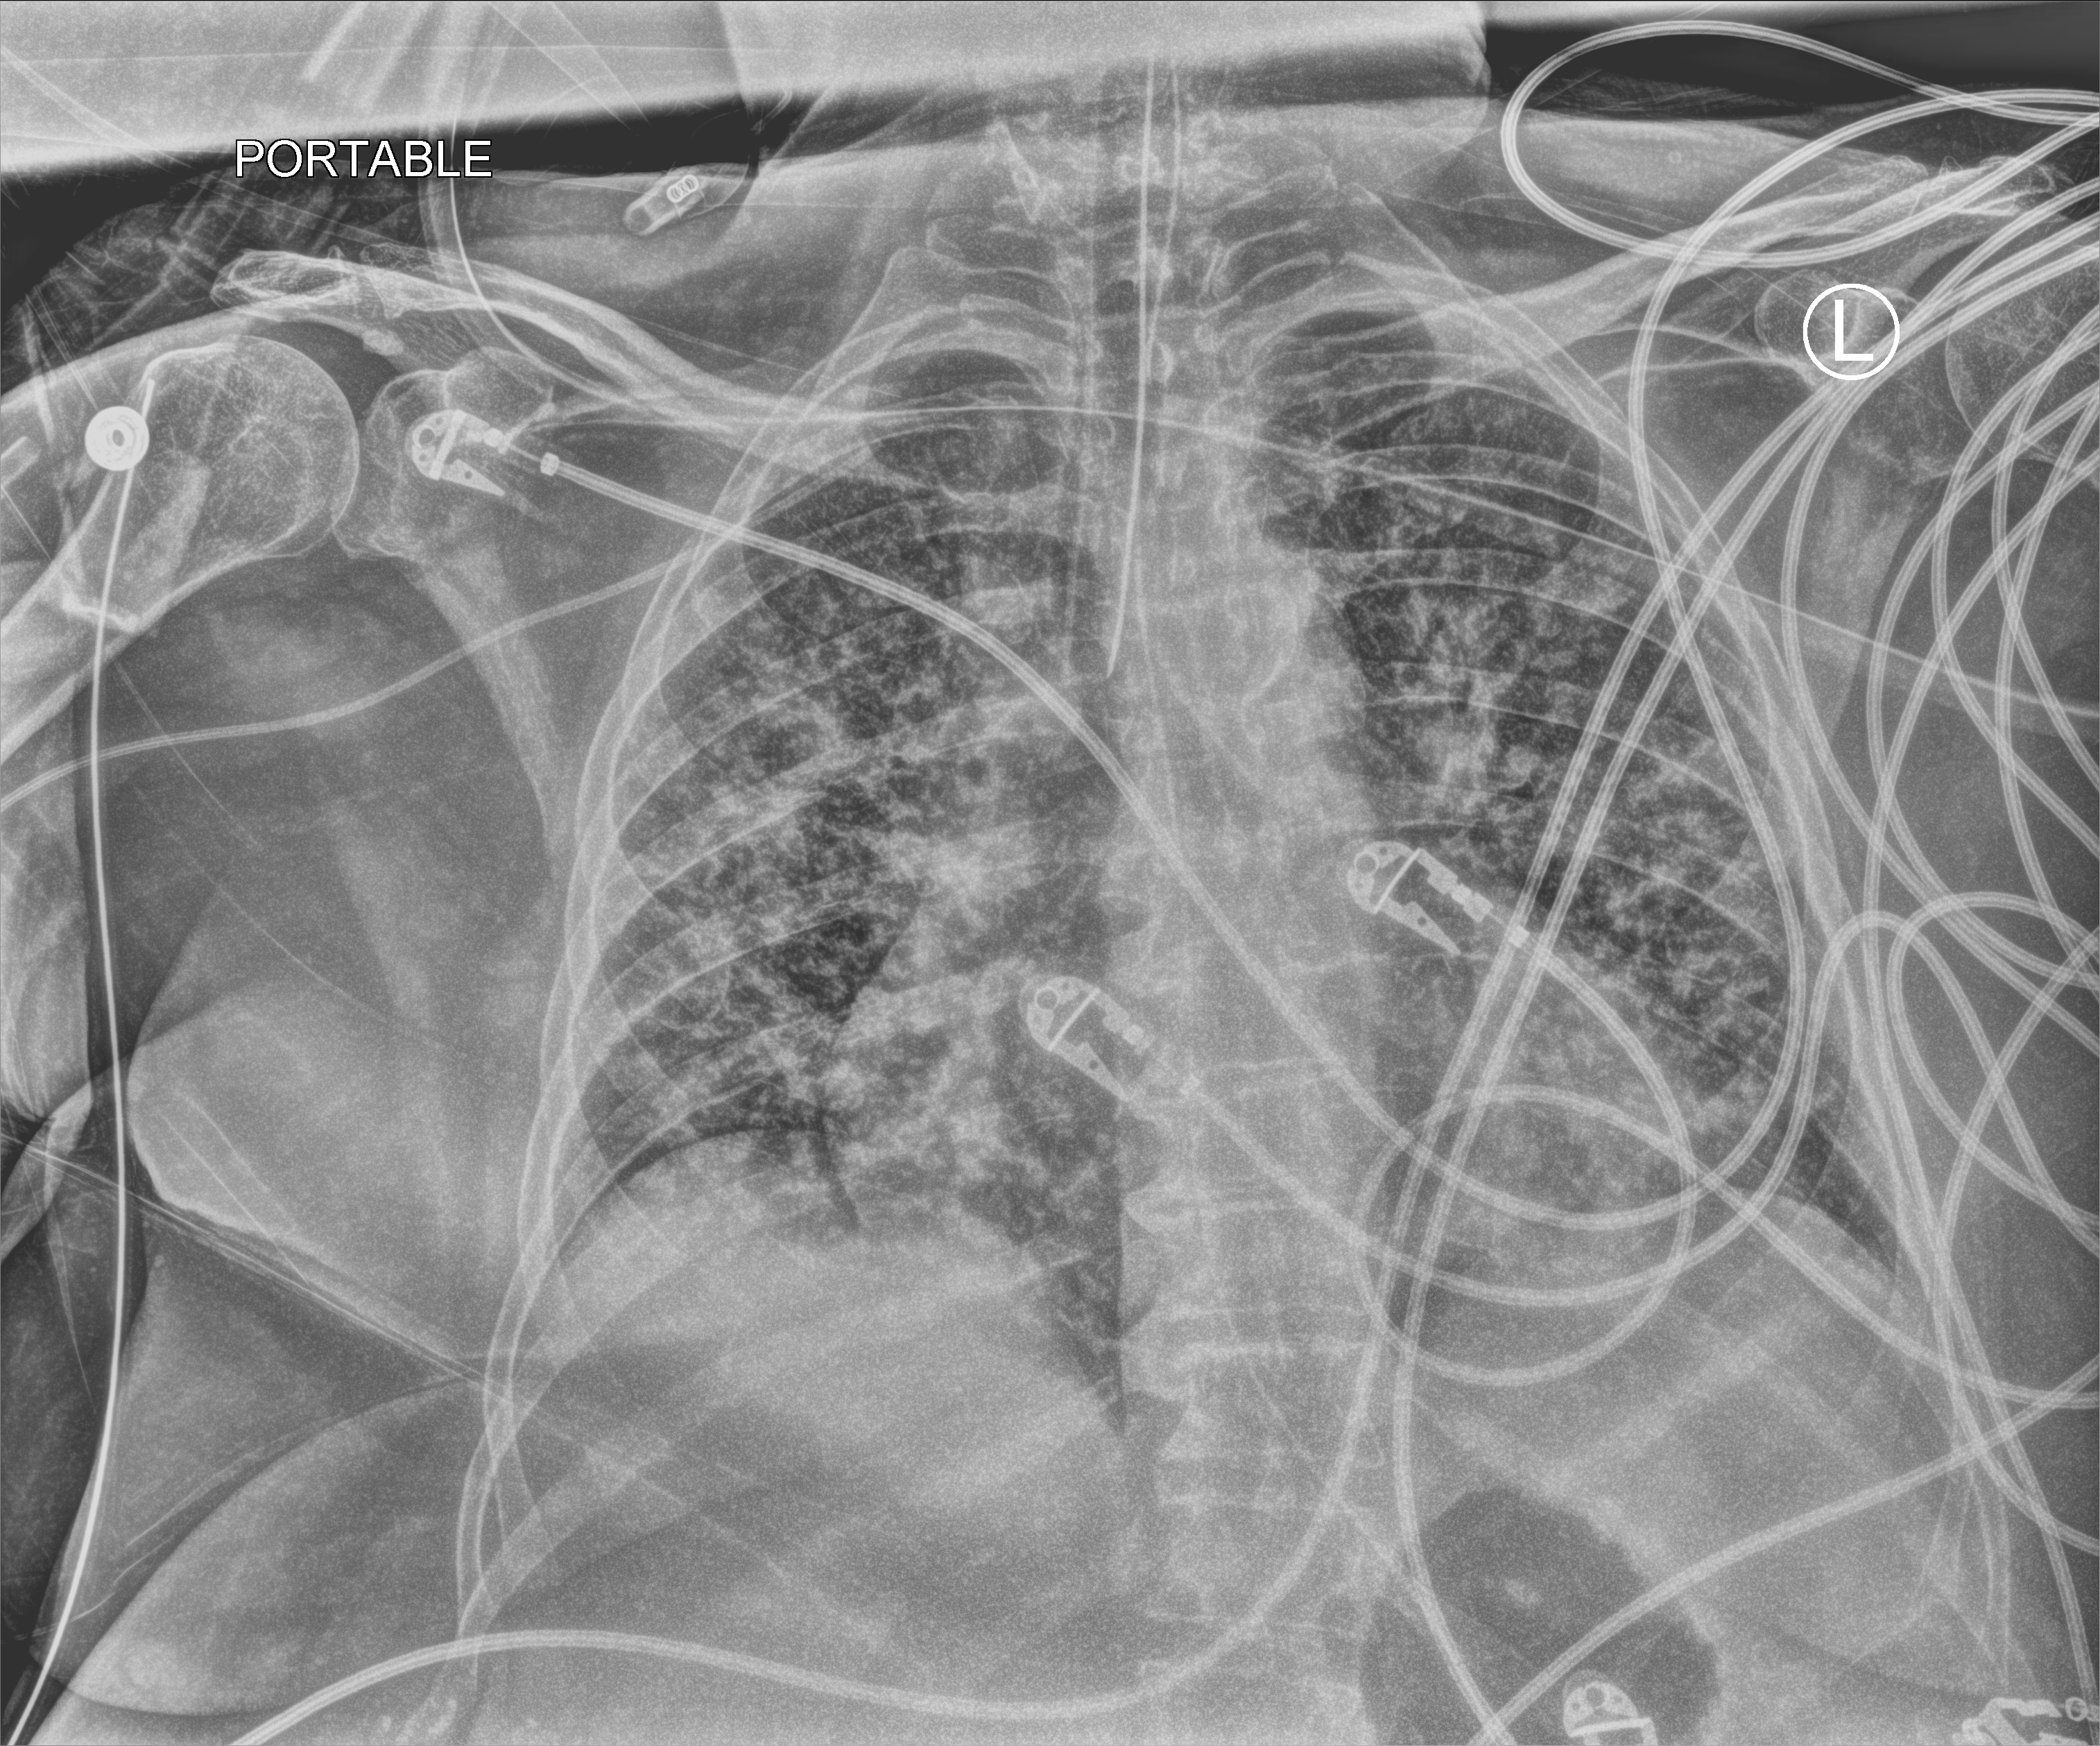
Bedside chest radiograph (computed radiography). Patient hospitalised with COVID-19; female, aged 75–90 years.
From the hospital-stay record, not from the radiograph (when in the stay this image was taken is not recorded): mechanically ventilated during this hospital stay: yes; length of hospital stay: 31 days; hypertension (admission record): yes.